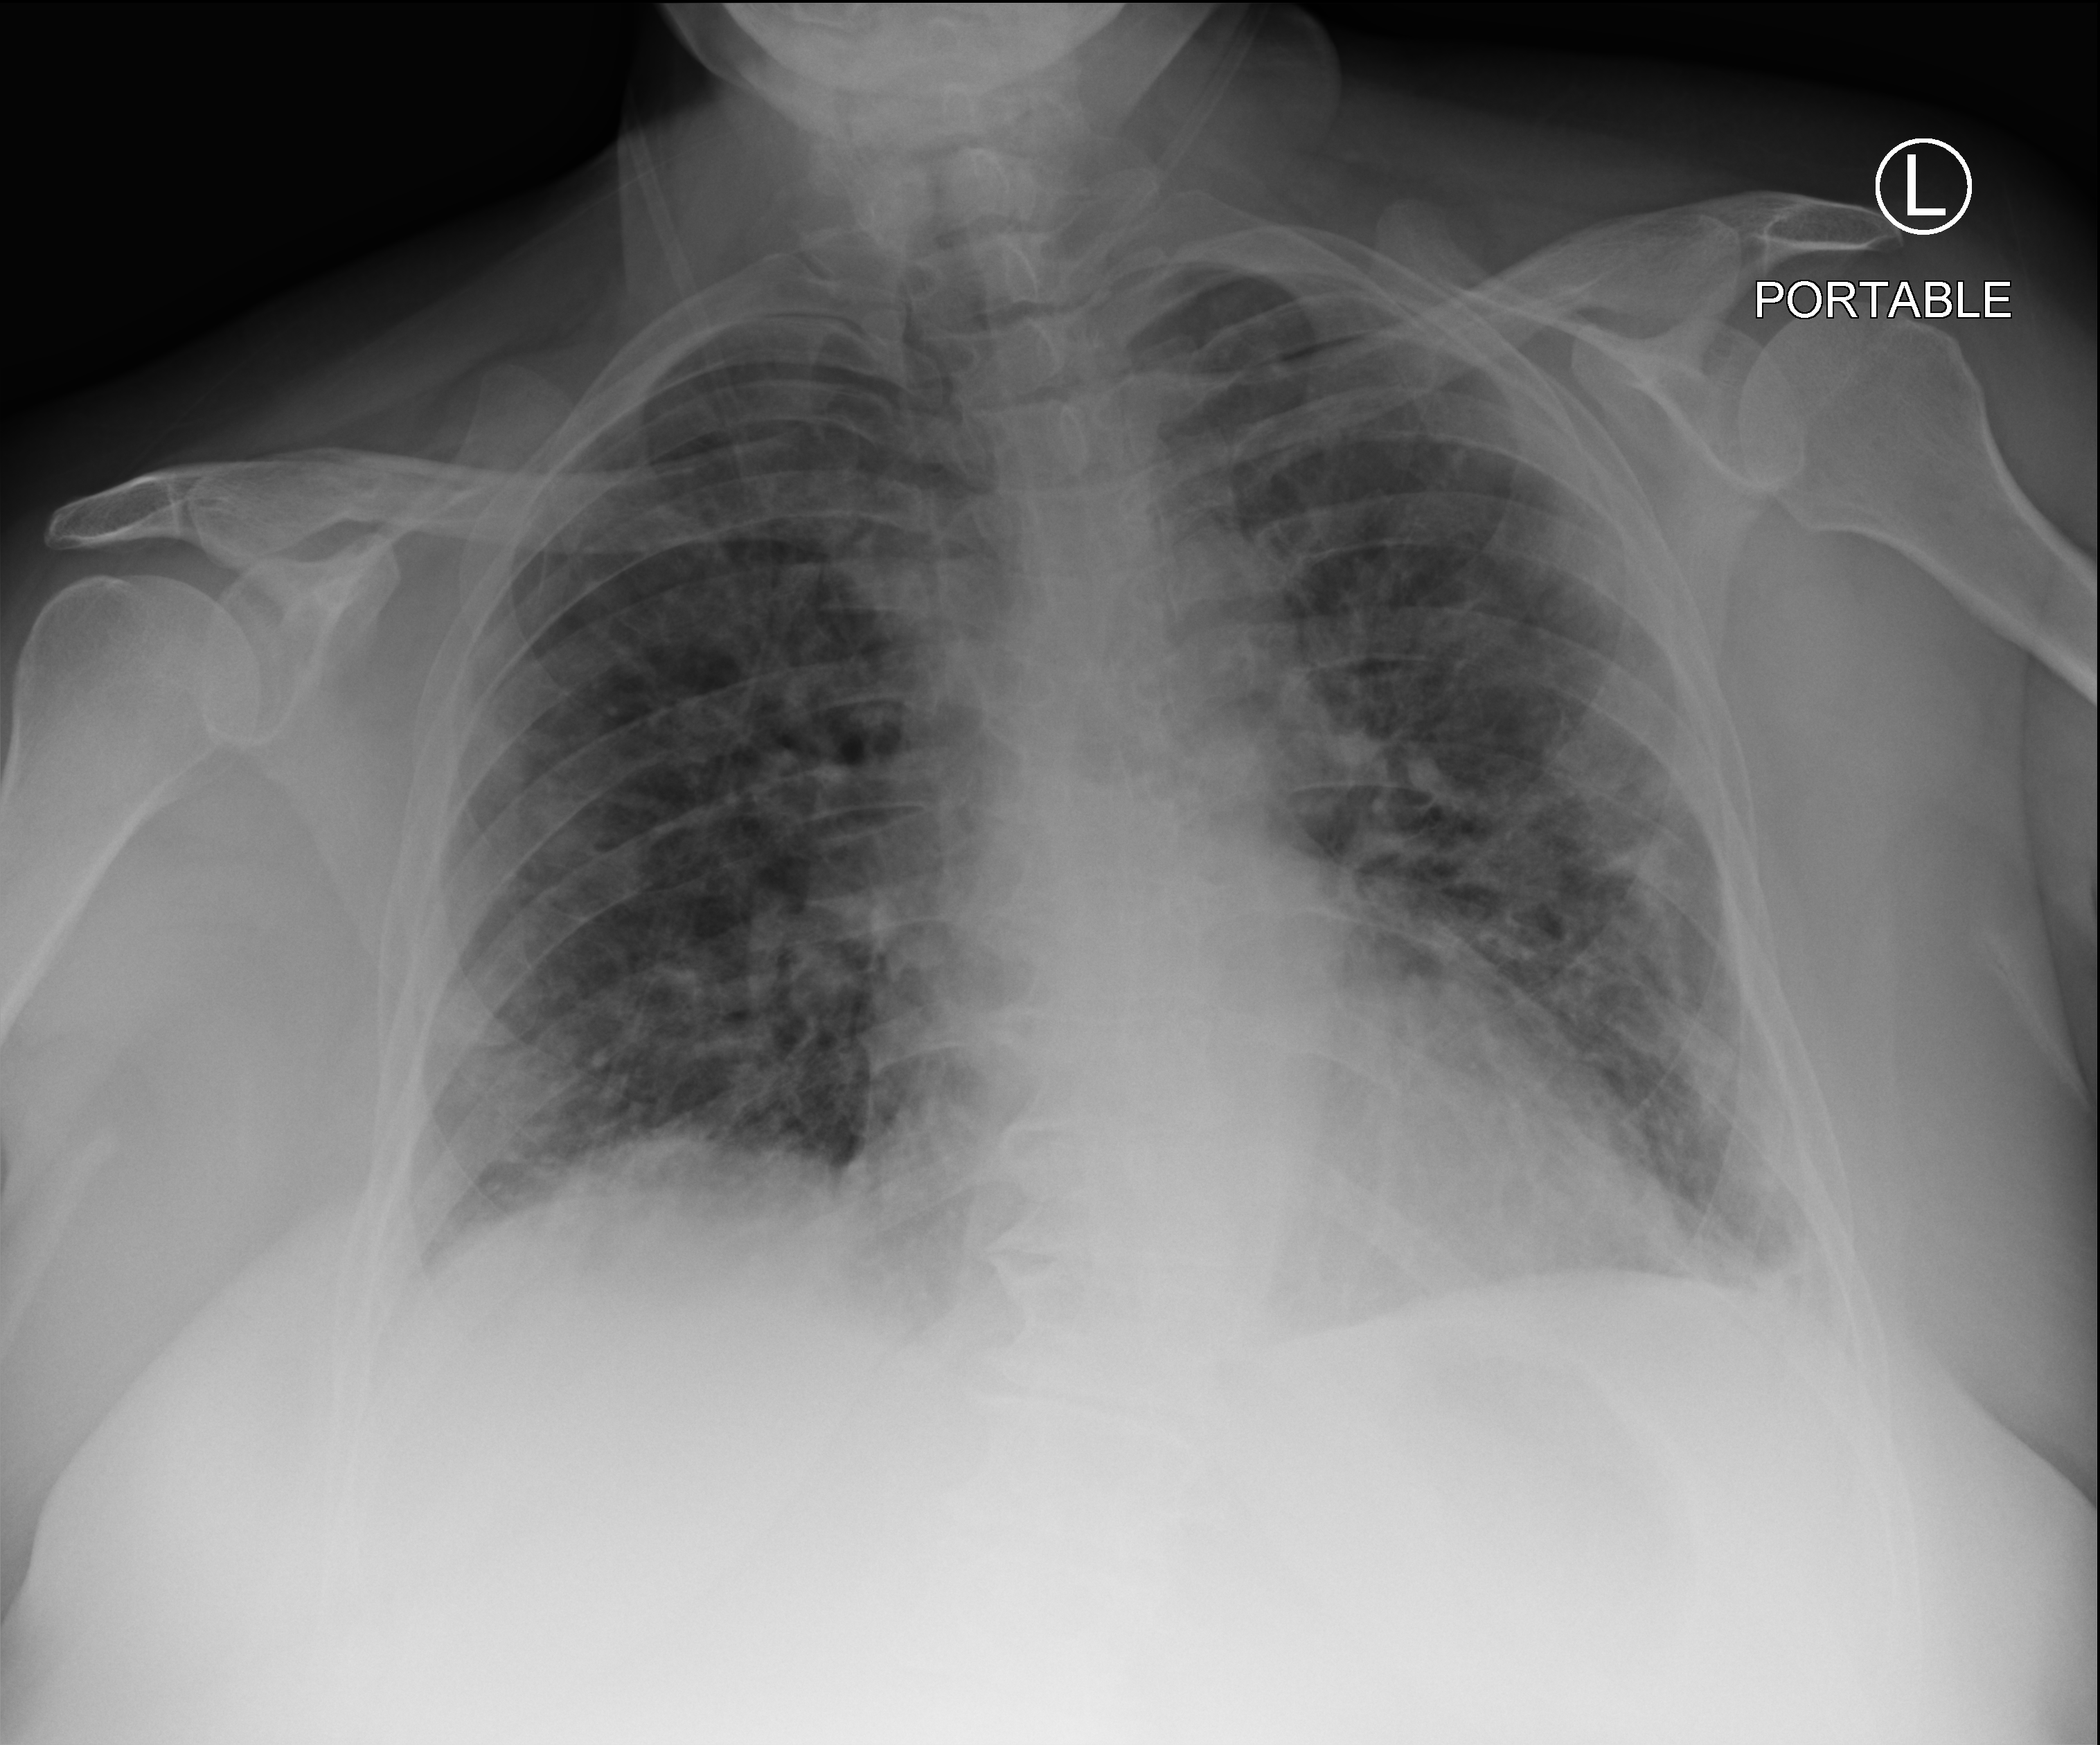
Portable chest radiograph; anteroposterior (AP) projection. Patient hospitalised with COVID-19; female, aged 60–74 years.
From the hospital-stay record, not from the radiograph (when in the stay this image was taken is not recorded): length of hospital stay: 7 days; admitted to intensive care during this hospital stay: no; mechanically ventilated during this hospital stay: no.